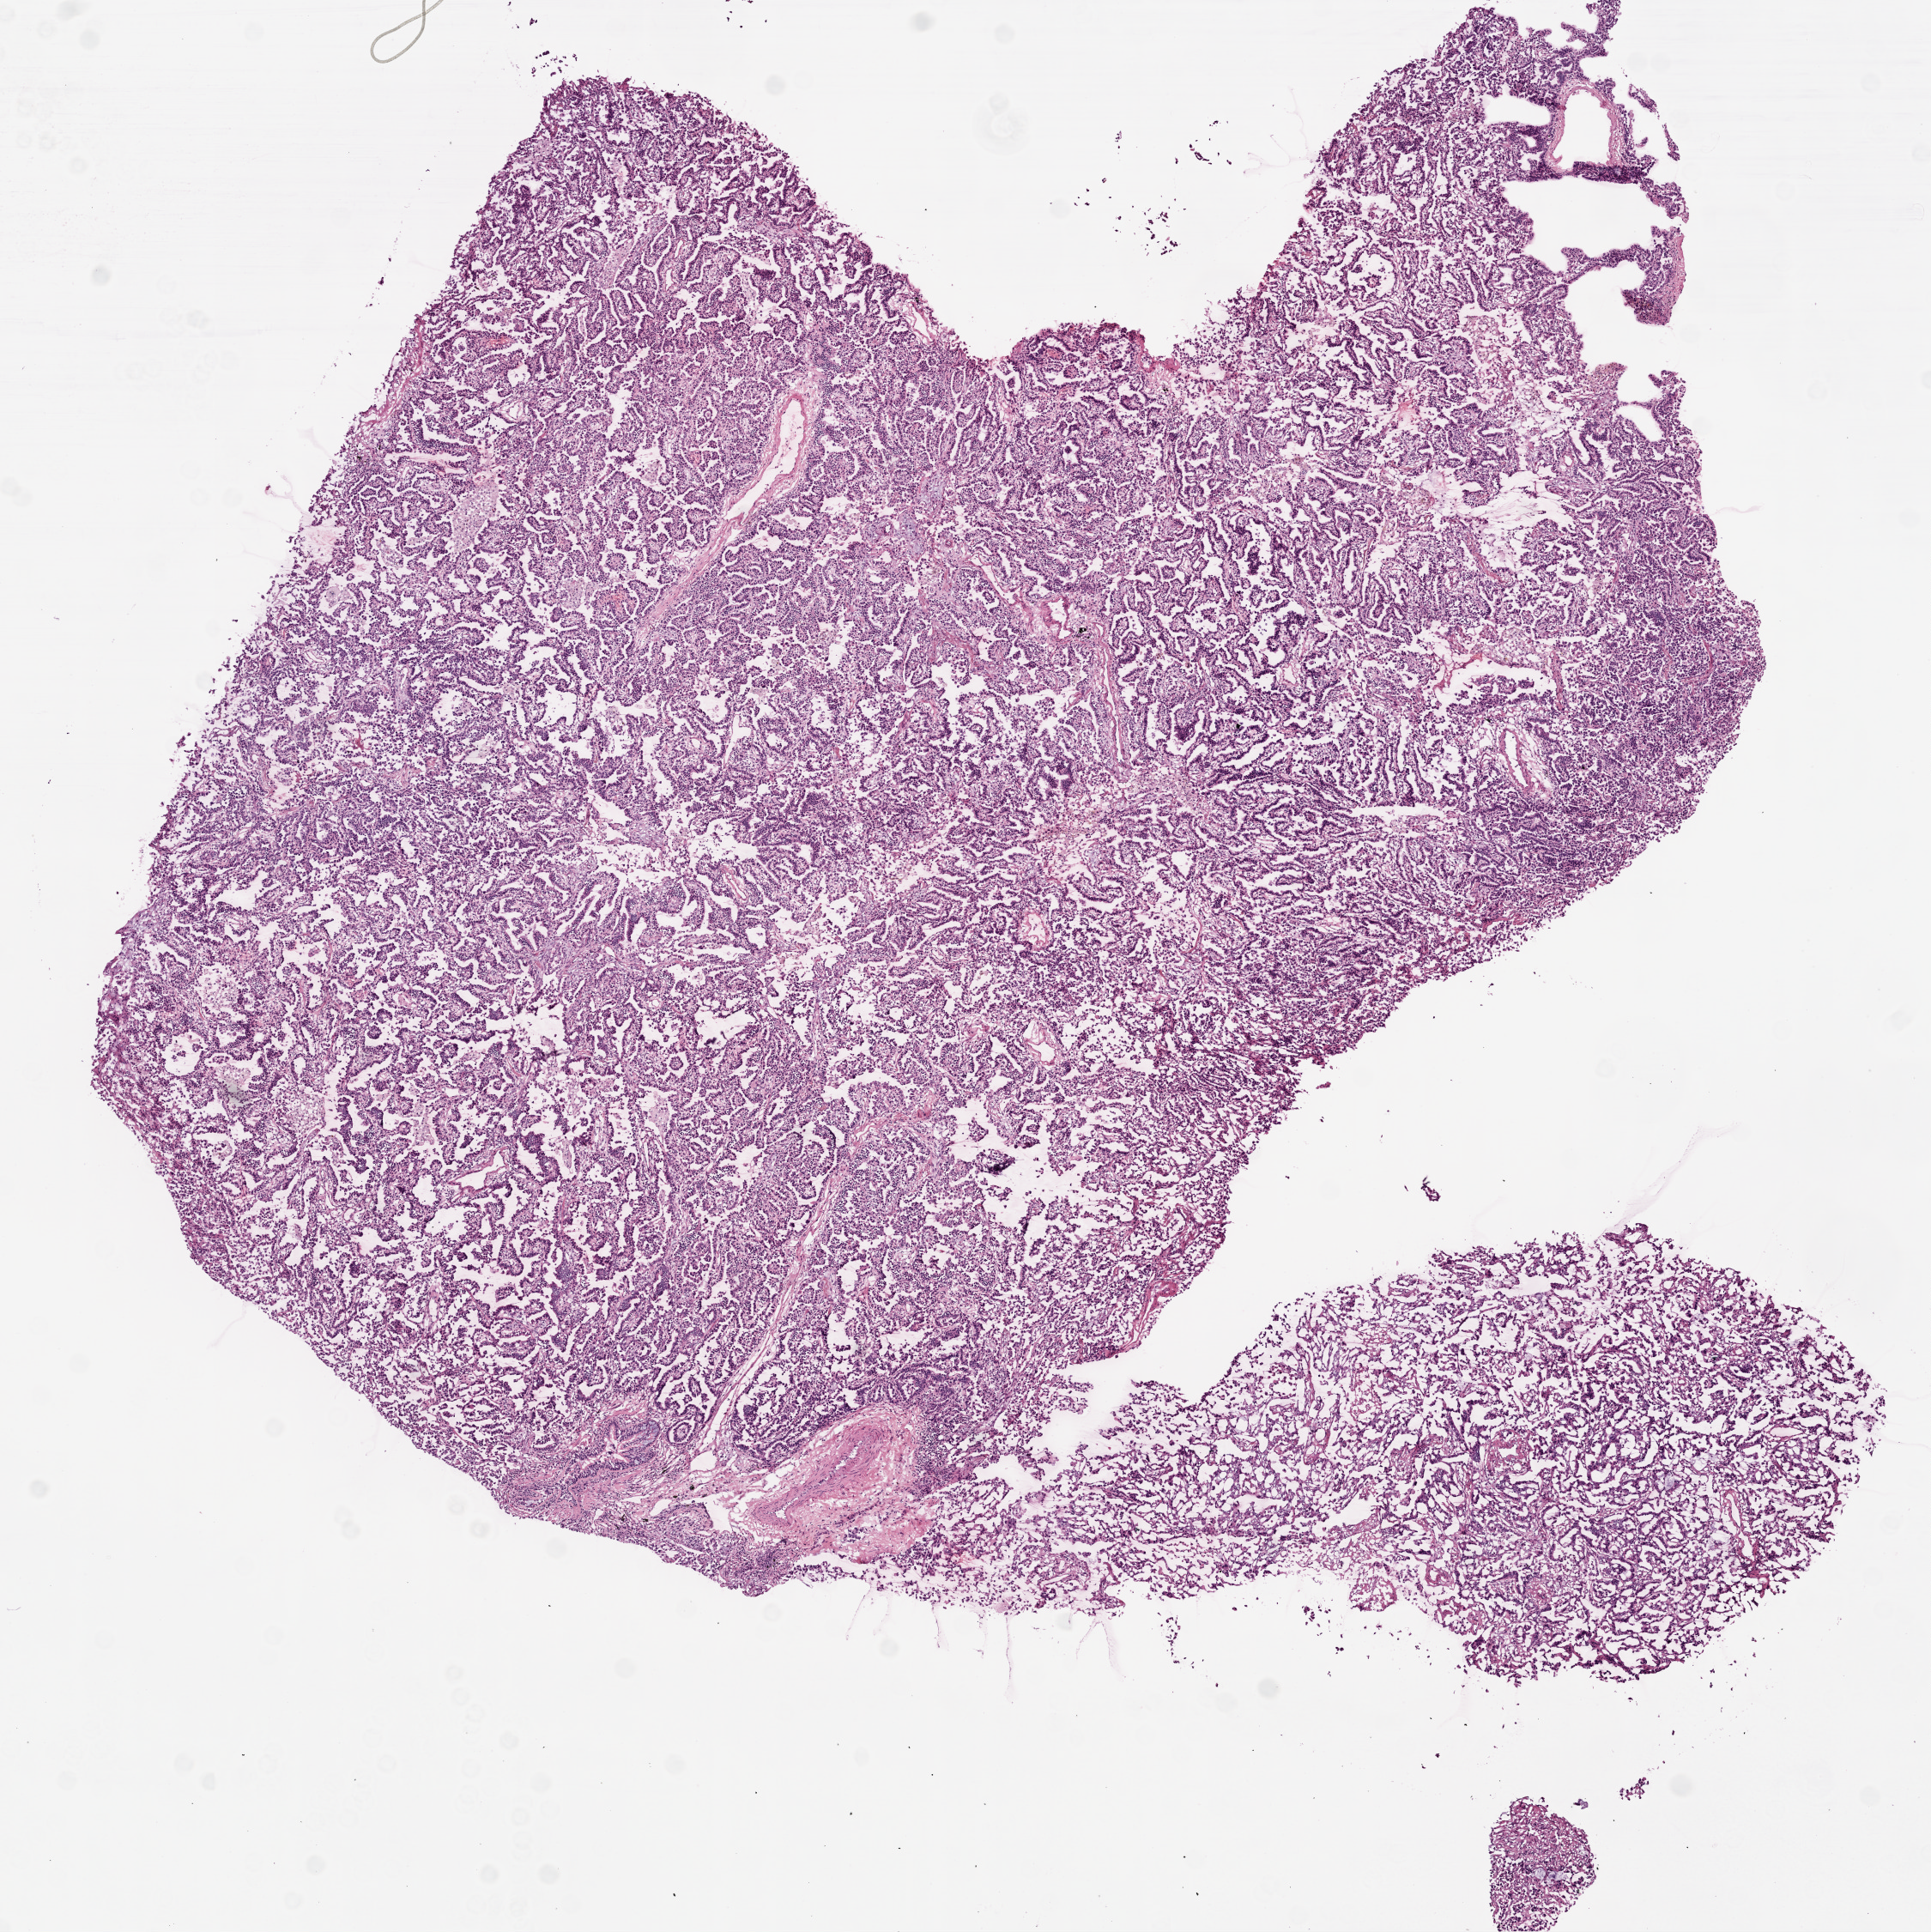
H&E whole-slide image, a low-resolution overview of the entire scanned area, about 9.0 x 9.0 mm (from a 20x scan); frozen section from the top of the tissue portion; lung, primary tumour sample. Patient: female, age at initial diagnosis 51 years. Pathologist review of this section (percent, as recorded): tumour cells 95%, tumour nuclei 75%.
Diagnosis: Adenocarcinoma, NOS (upper lobe, lung).